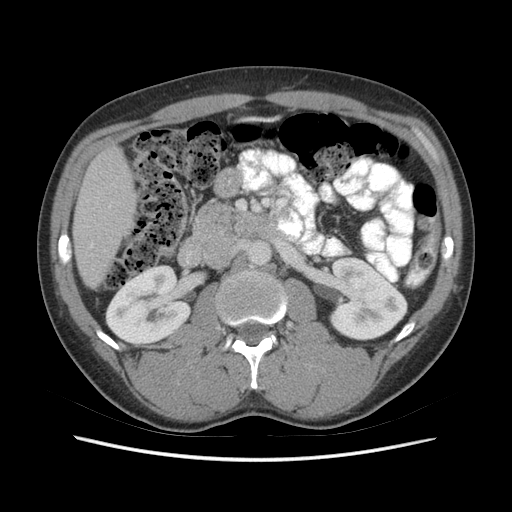
Contrast-enhanced abdominal CT (liver protocol), one axial slice; slice 17 of 73 in the series (ordered by position); 140 kVp; soft-tissue window (W 400 / L 40 HU); 2.5 mm slice thickness; 512 × 512 image matrix, field of view 360 × 360 mm. From the clinical record (not read from this slice): diagnosis: hepatocellular carcinoma (patient treated with transarterial chemoembolisation; whether this scan precedes or follows treatment is not stated here); TNM stage (as recorded): Stage-IIIA; Child-Pugh class: A; tumour nodularity: multinodular; tumour size: 6.6 cm.
Annotated regions visible in this slice (semi-automatic segmentation, software-assisted and operator-edited):
- liver parenchyma outside the tumour (the mass and vessels are separate outlines, so this box may not span the whole liver): box from (x=72, y=146) to (x=136, y=288) px